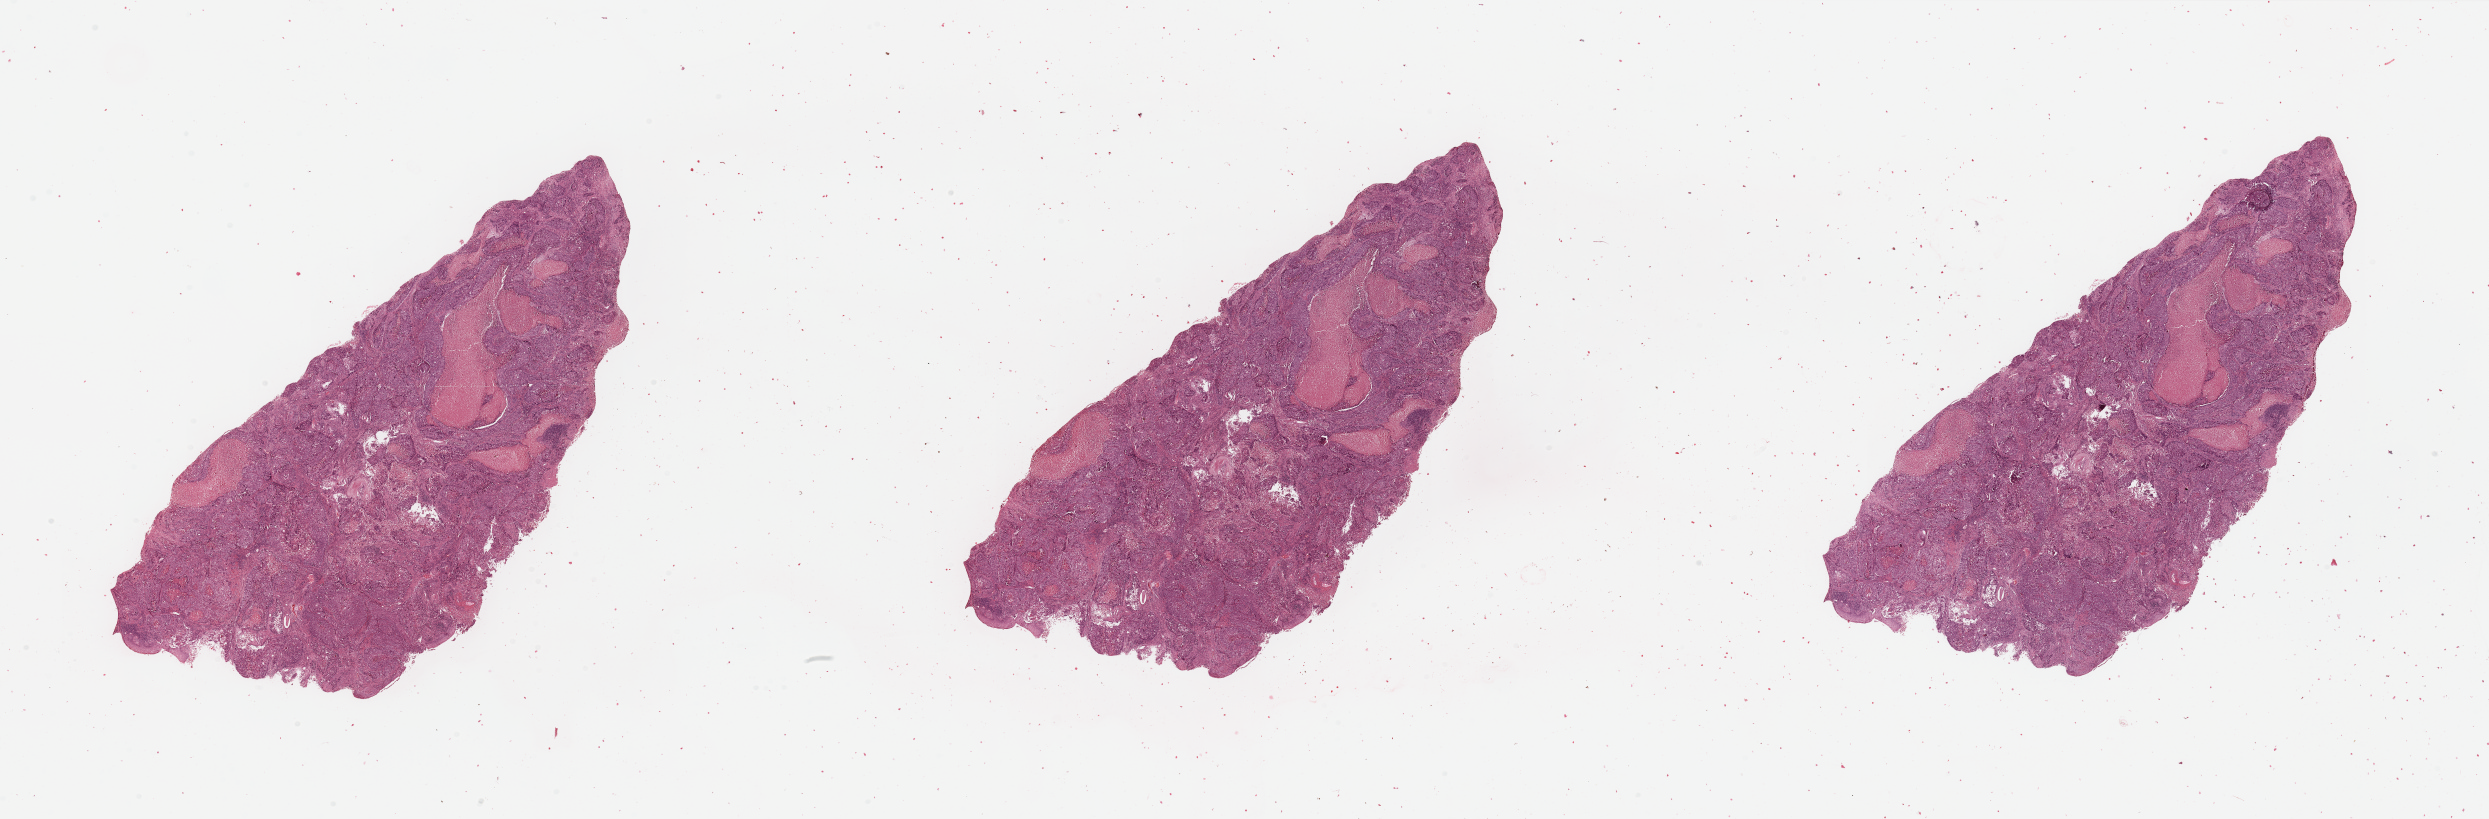
Whole-slide histology image, H&E — whole scanned area (about 39.4 x 13.0 mm) shown as a low-resolution overview. Head and neck, tissue type not recorded. 64-year-old male patient.
* patient diagnosis: Squamous cell carcinoma, NOS (larynx, NOS)